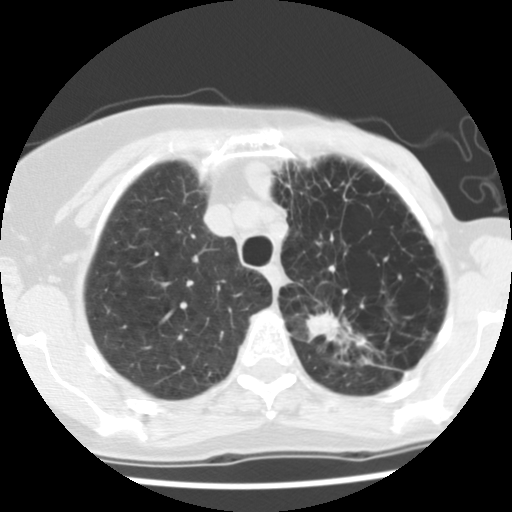
Low-dose screening chest CT, one axial slice; position 102 of 128 along the scan axis; reconstruction kernel STANDARD; 140 kVp; lung window (W 1500 / L -600 HU); 512 × 512 image matrix, field of view 290 × 290 mm.
Outlined on this slice (expert manual segmentation):
- lesion 1 (tumor, upper lobe of left lung): box from (x=306, y=311) to (x=369, y=349) px